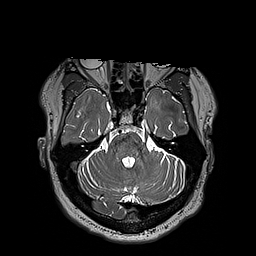
Brain MRI from a brain-tumour surgery series, one axial slice. 1 mm slice thickness. 256 × 256 image matrix, field of view 250 × 250 mm. Case-level facts recorded for this patient, not image findings: histopathology: Astrocytoma; WHO grade: 3; IDH mutation: yes; tumour location: Left Insular.
Structures marked on this image (expert manual segmentation):
- tumour: bounding box (x1, y1, x2, y2) in pixels: (150, 98, 162, 107)